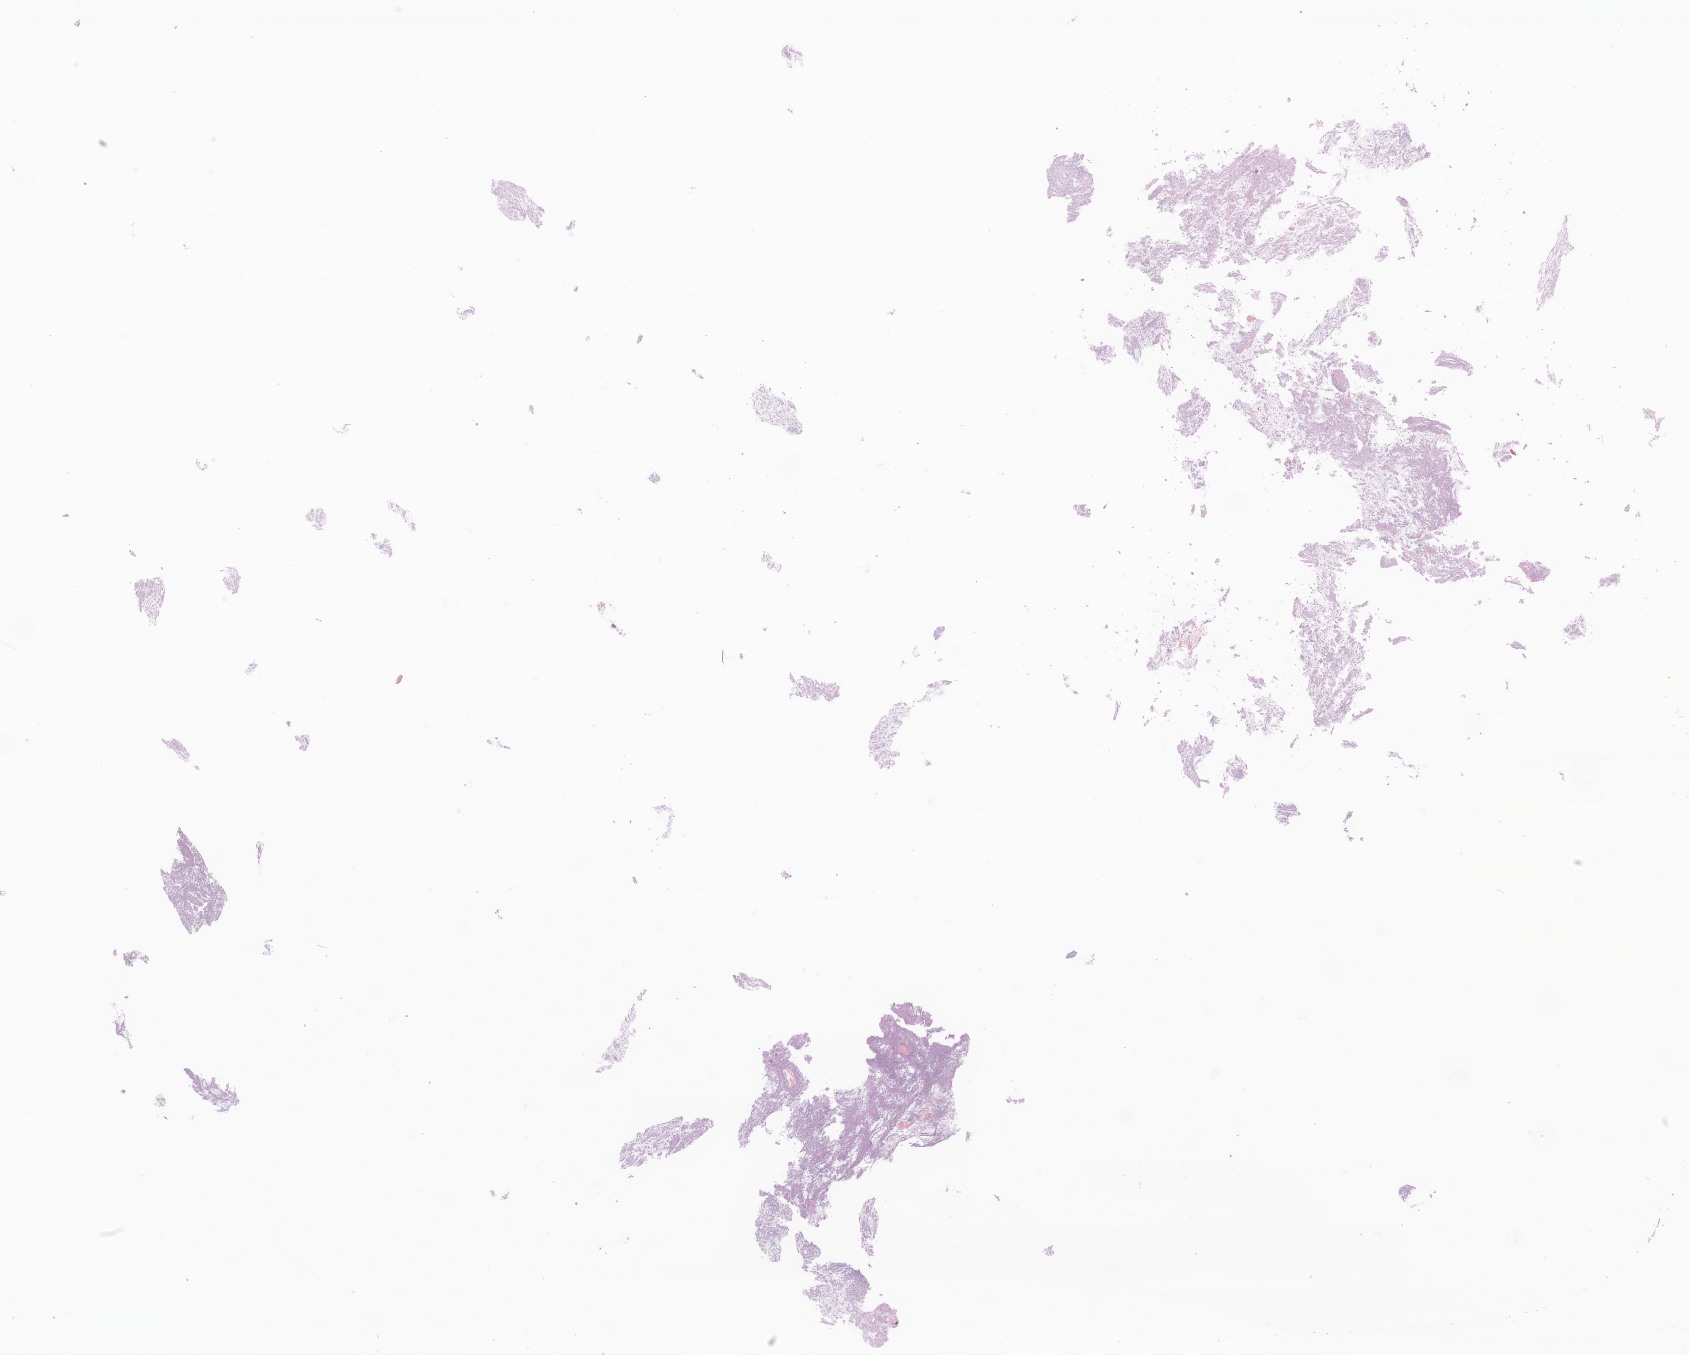
Haematoxylin and eosin whole-slide image of tumor tissue from the brain — a low-resolution overview of the entire scanned area, about 28.5 x 22.9 mm, formalin-fixed paraffin-embedded section. Patient: female, age 204 months.
Recorded diagnosis: Neoplasm, benign.